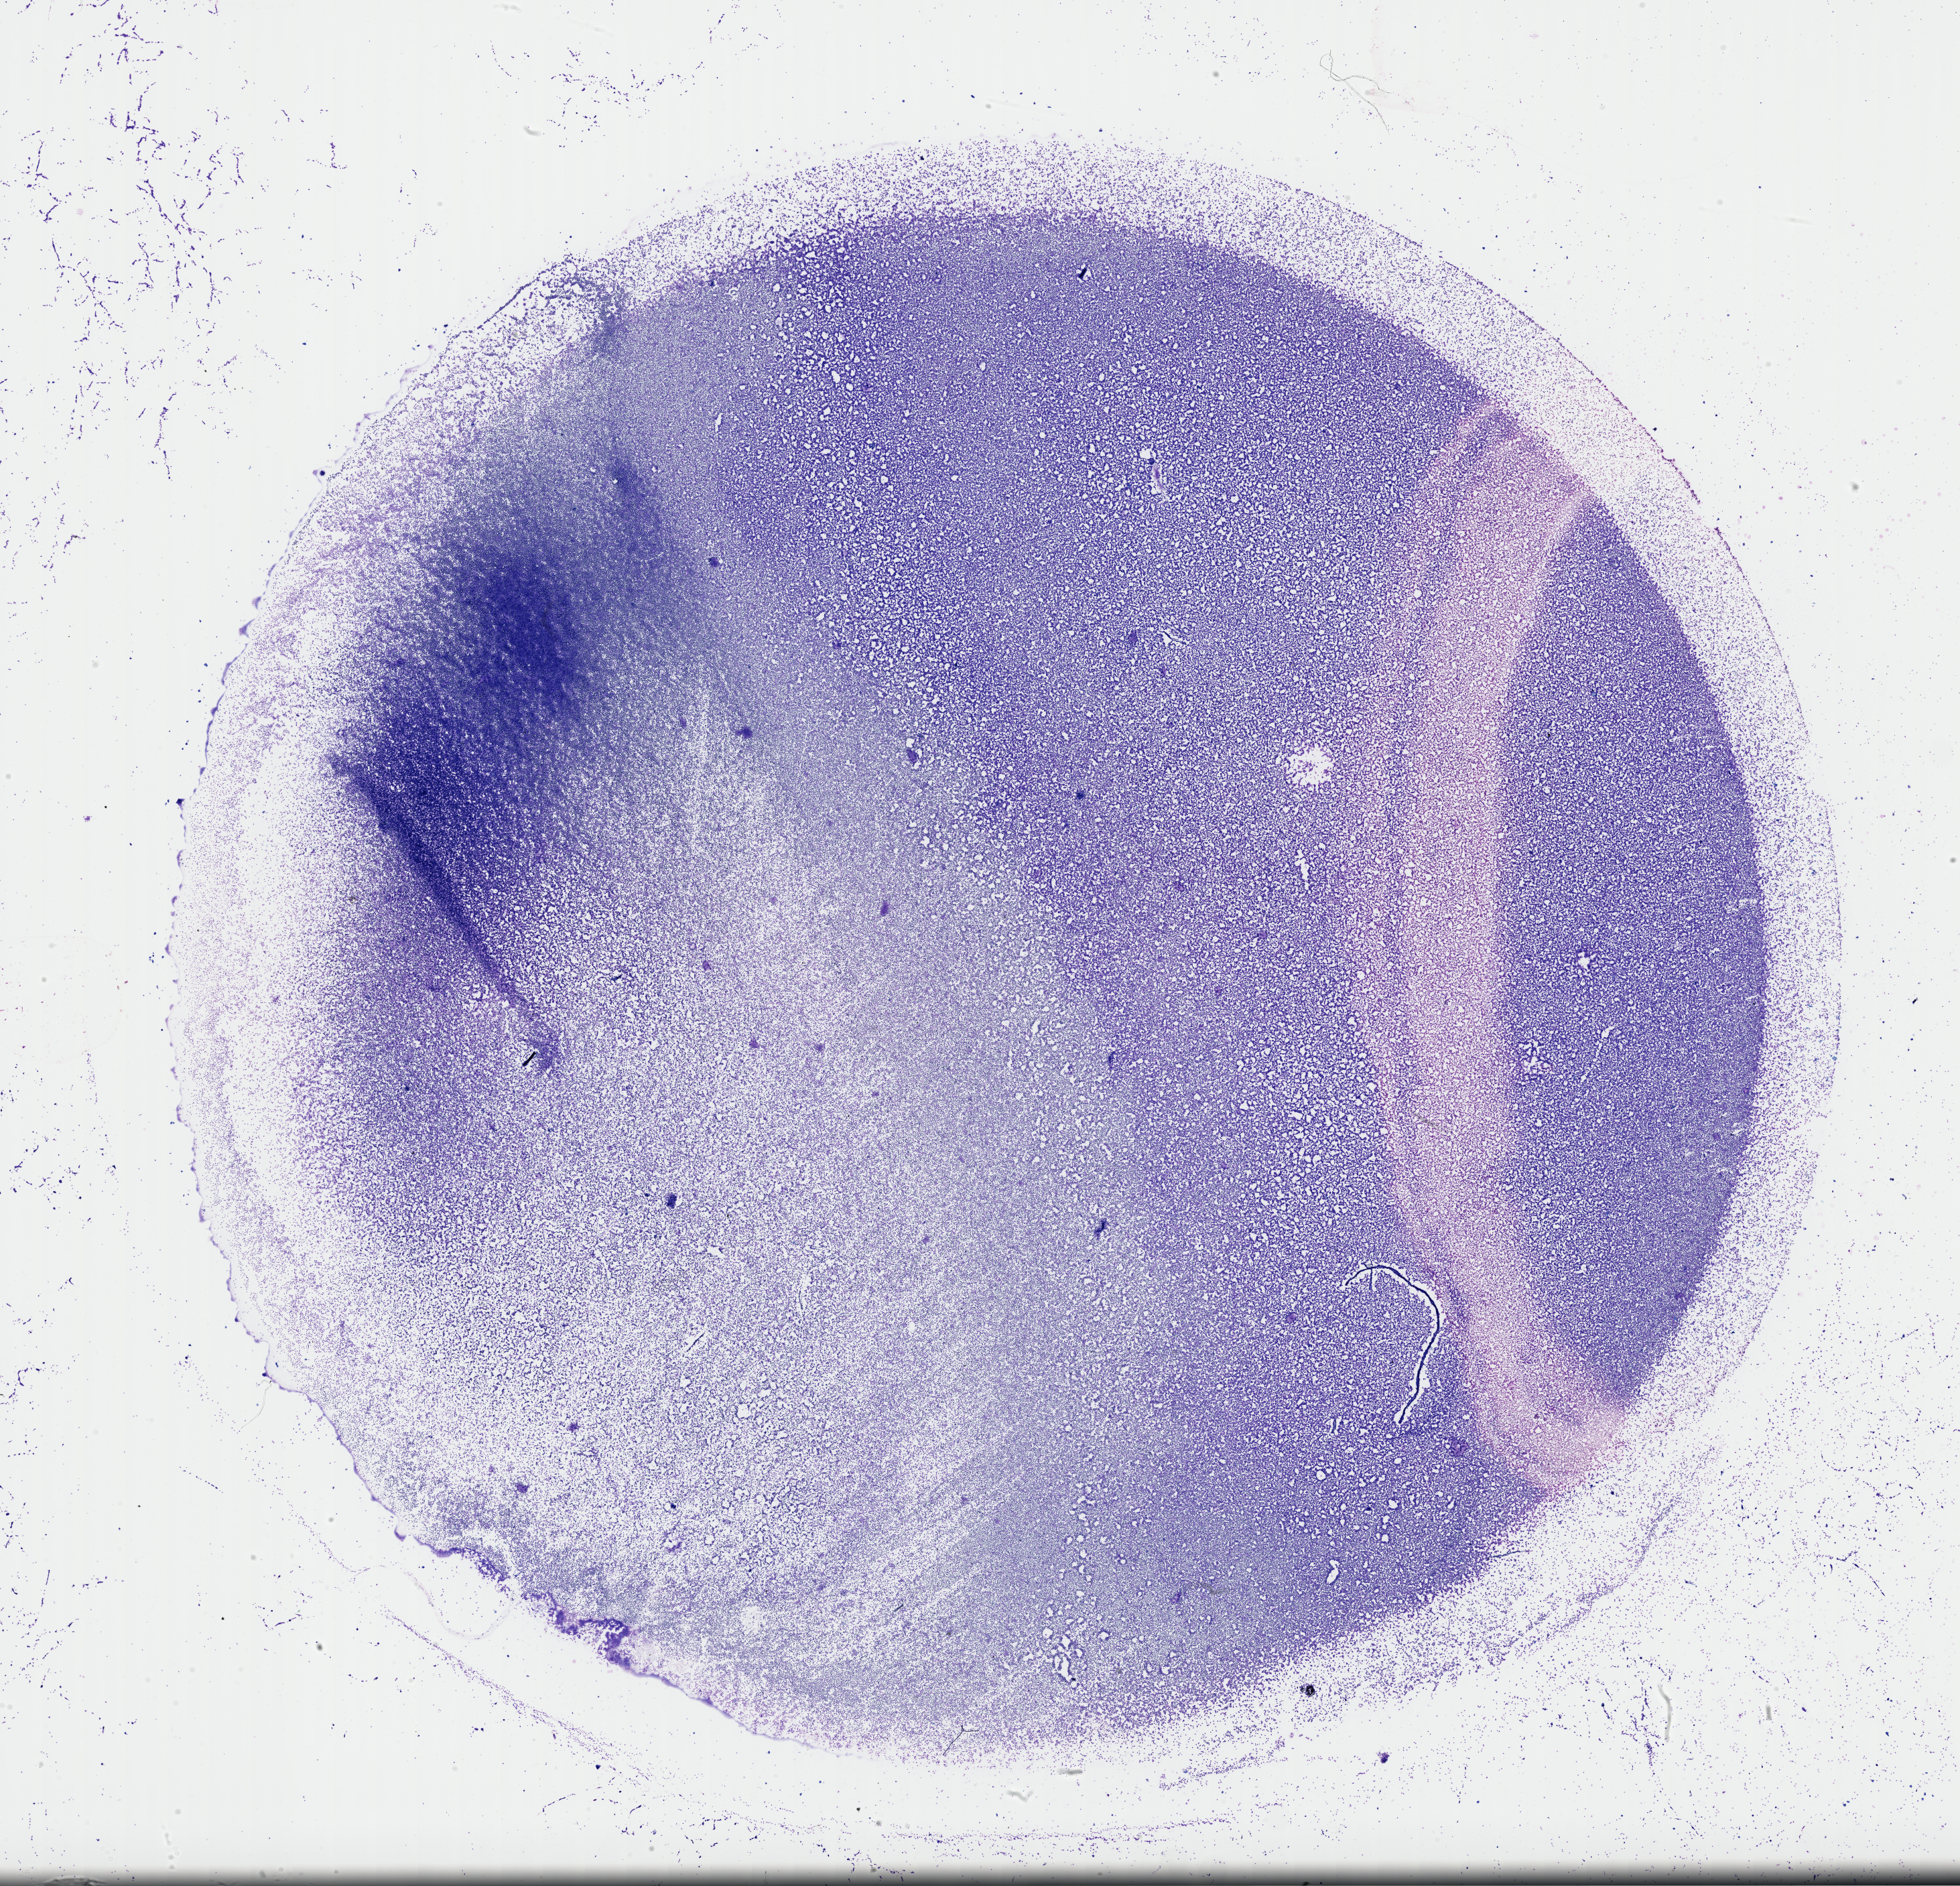
Hematoxylin and eosin (H&E) stained whole-slide image, a low-resolution overview of the entire scanned area, about 23.6 x 22.7 mm (slide scanned at 40x); bone marrow (leukaemic) sample. Female, 85 y/o. Blasts: 80%.
* WHO classification: AML with maturation
* FAB classification: M2
* diagnosis: Acute Myeloid Leukemia